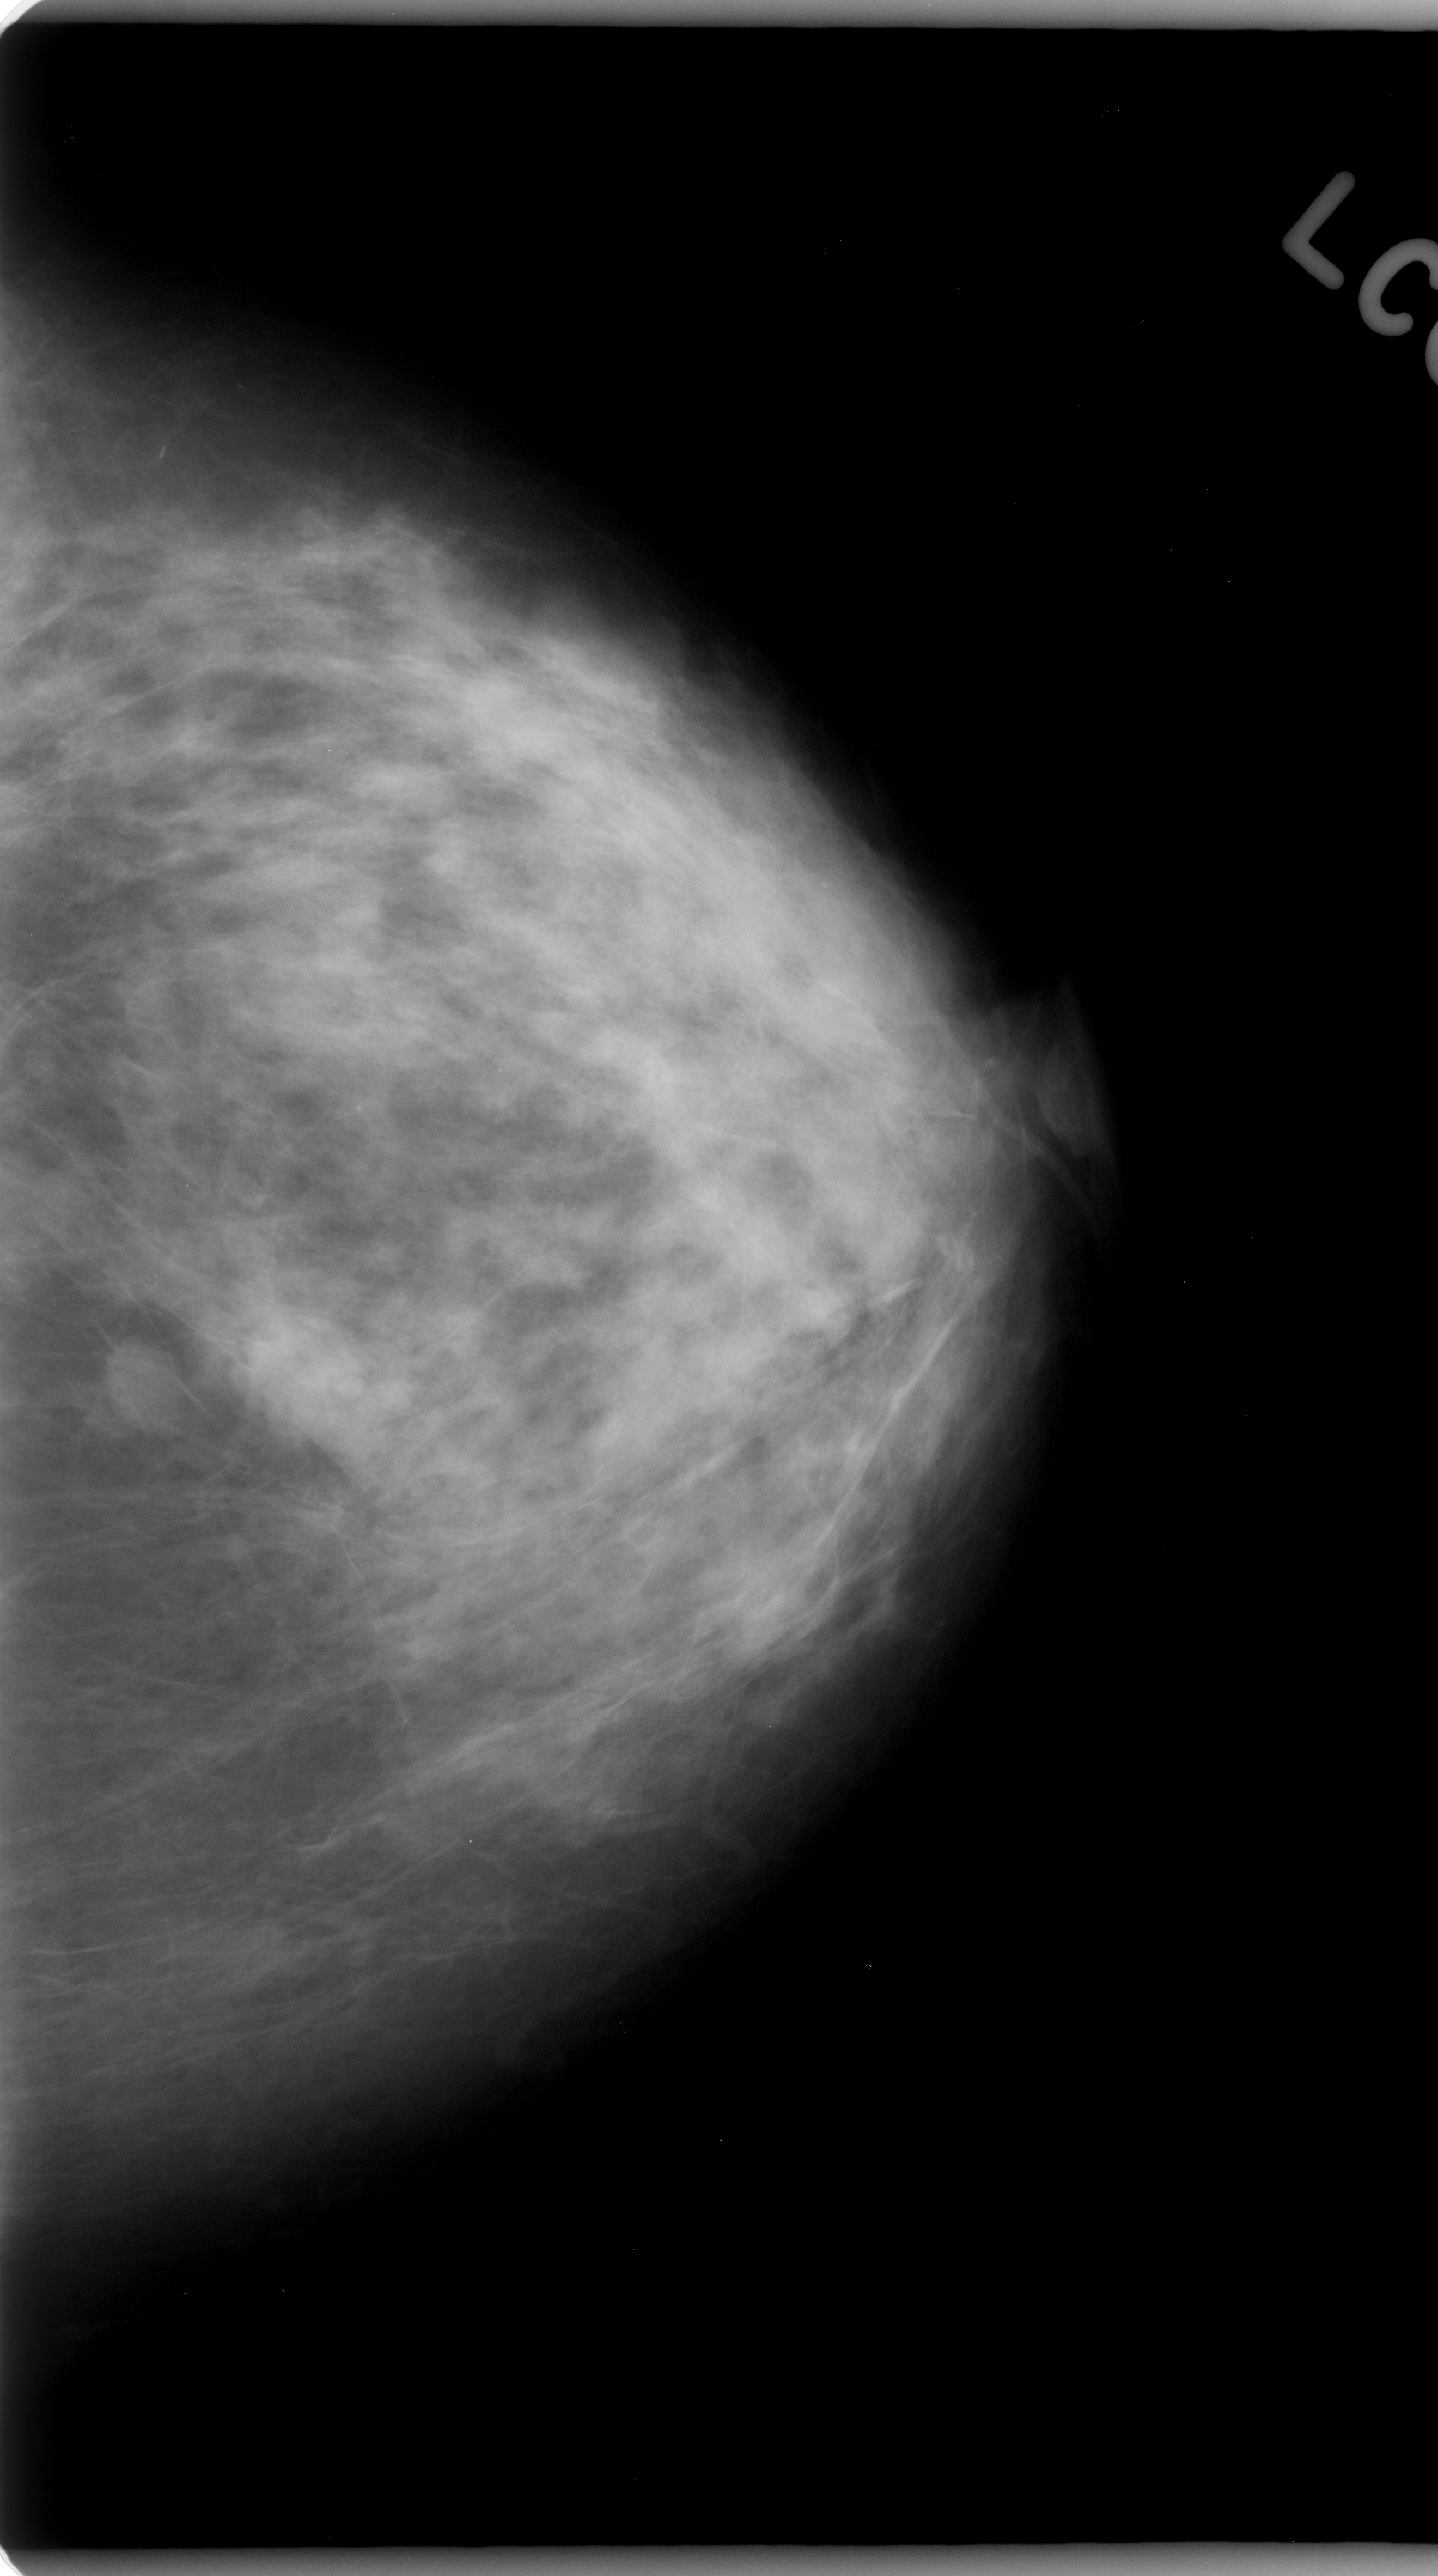
Mammogram (digitized film), left breast, CC view, BI-RADS breast density category 2 (scale 1–4).
Finding: mass, shape oval, margins circumscribed; BI-RADS assessment category 3; subtlety rating 5 on a 1 (subtle) to 5 (obvious) scale; pathology result (as recorded, not read from the image): benign.